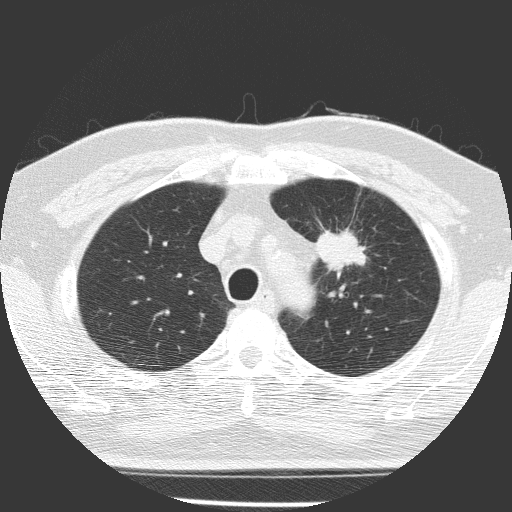
Chest CT (low-dose screening protocol), one axial image. Baseline screening round. Lung window (W 1500 / L -600 HU). 2 mm slice thickness. Lung (sharp) reconstruction kernel (FC51). 120 kVp. Slice 38 of 156 in the series. 512 × 512 image matrix. Male participant, aged 70 years at enrolment.
Lesion marked by an expert reader, bounding box (x1, y1, x2, y2) in pixels: (297, 219, 373, 292). The screening reader recorded 3 non-calcified nodules or masses ≥4 mm on this exam; which of them this box marks is not recorded.